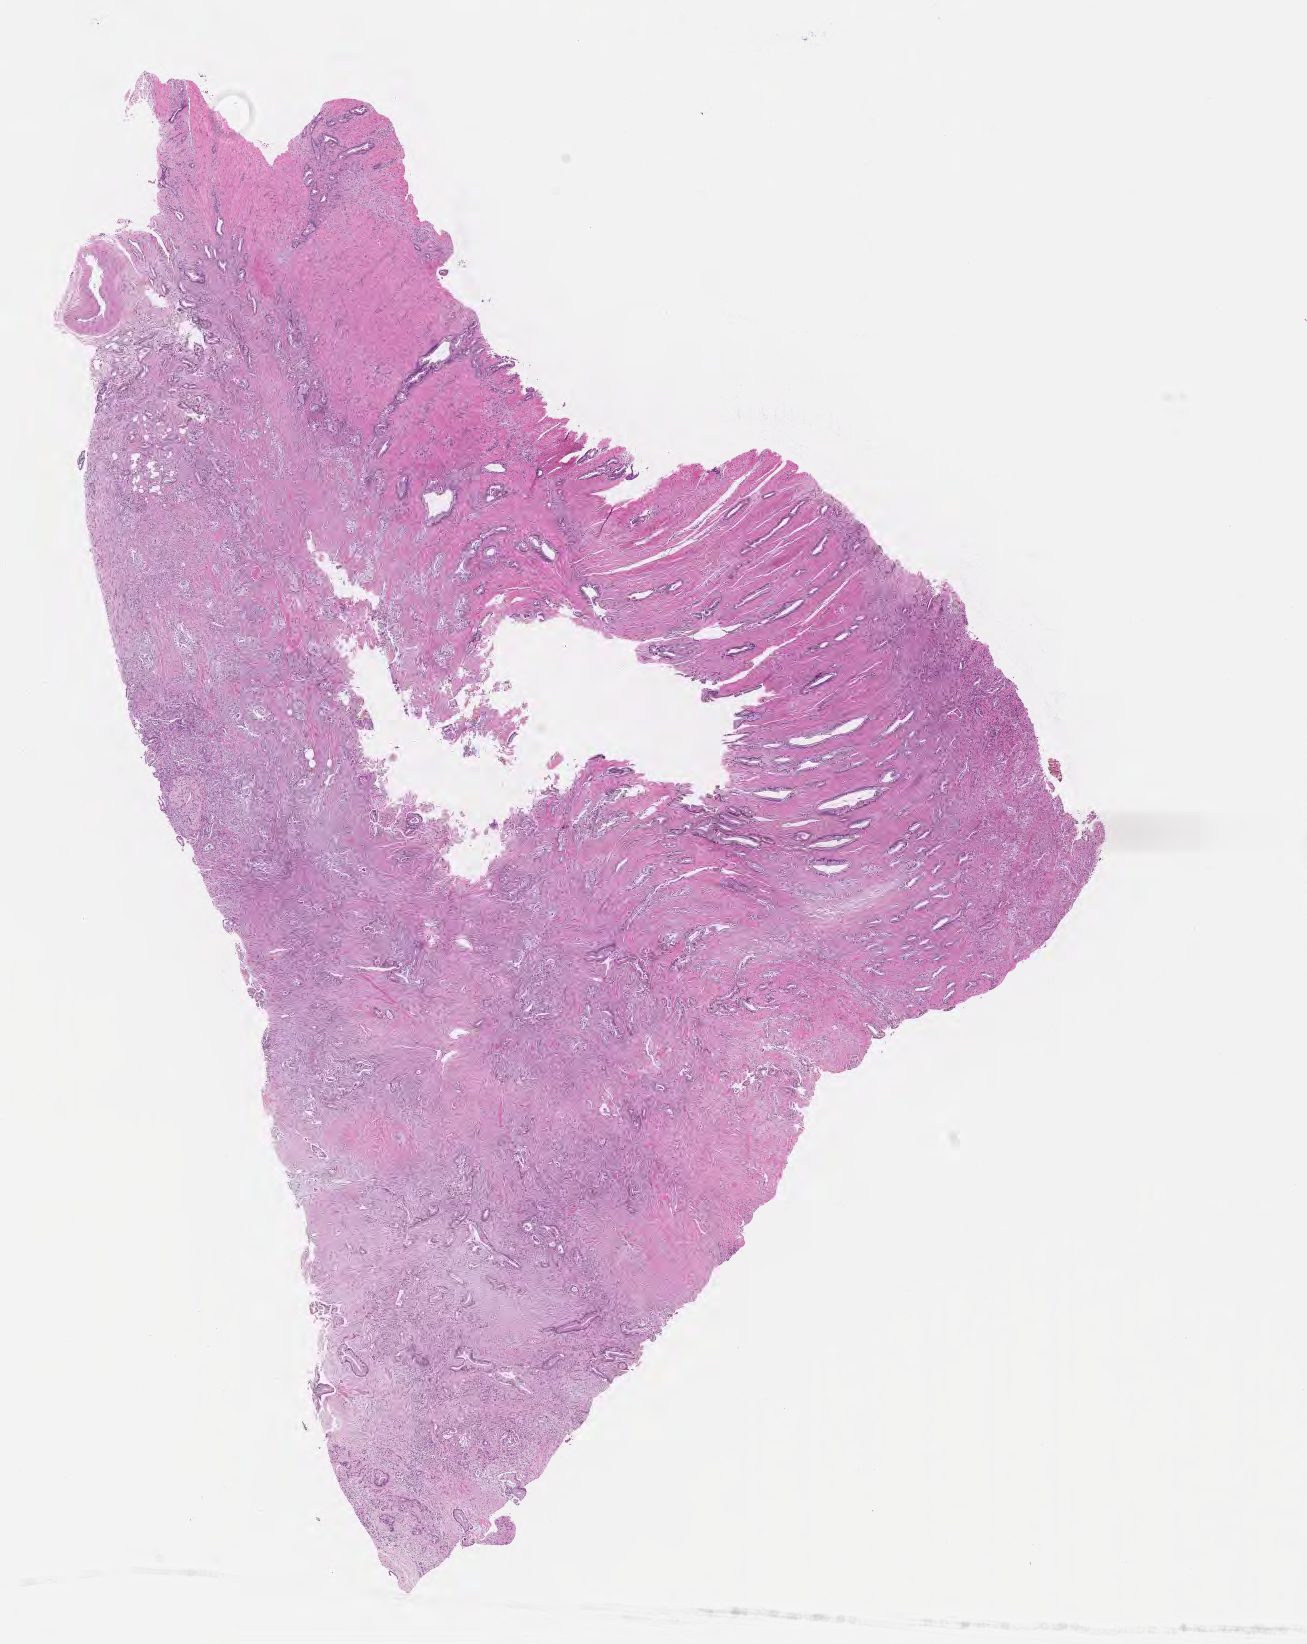
Whole-slide image, haematoxylin and eosin stain, whole scanned area (about 10.6 x 13.3 mm) shown as a low-resolution overview, FFPE section, primary tumor, anatomic site: head of pancreas. Patient: male, age at initial diagnosis 63 years. Tumor grade: G2 (moderately differentiated). Composition of this section per pathologist review: tumor cells 35%, tumor nuclei 50%, stromal cells 30%, necrosis 0%, normal cells 35%. Infiltration values recorded for this section: lymphocyte infiltration 0%, monocyte infiltration 0%, neutrophil infiltration 0%.
AJCC pathologic stage: Stage IB. Histologic diagnosis: Infiltrating duct carcinoma, NOS.